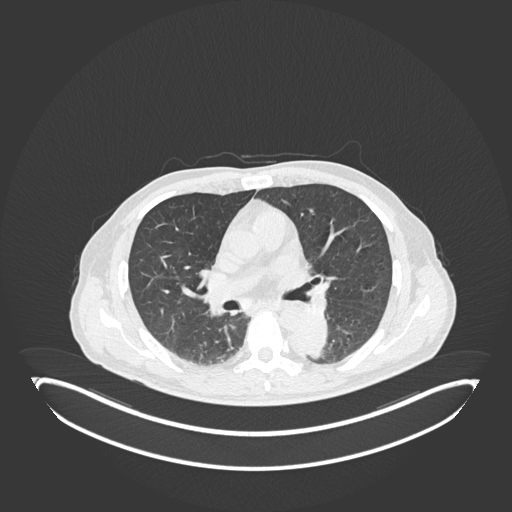
Chest CT, one axial slice; position 114 of 251 along the scan axis; reconstruction kernel B30f; 120 kVp; lung window (W 1500 / L -600 HU); 512 × 512 image matrix, field of view 500 × 500 mm. Patient: male, 72 years. Case-level facts recorded for this patient, not image findings: clinical TNM (as recorded): T2b N0 M1.
Annotated regions visible in this slice (rectangle marked by the reading radiologist):
- lung tumour (recorded histology: adenocarcinoma): bounding box <289,312,328,361> (left, top, right, bottom; pixels)